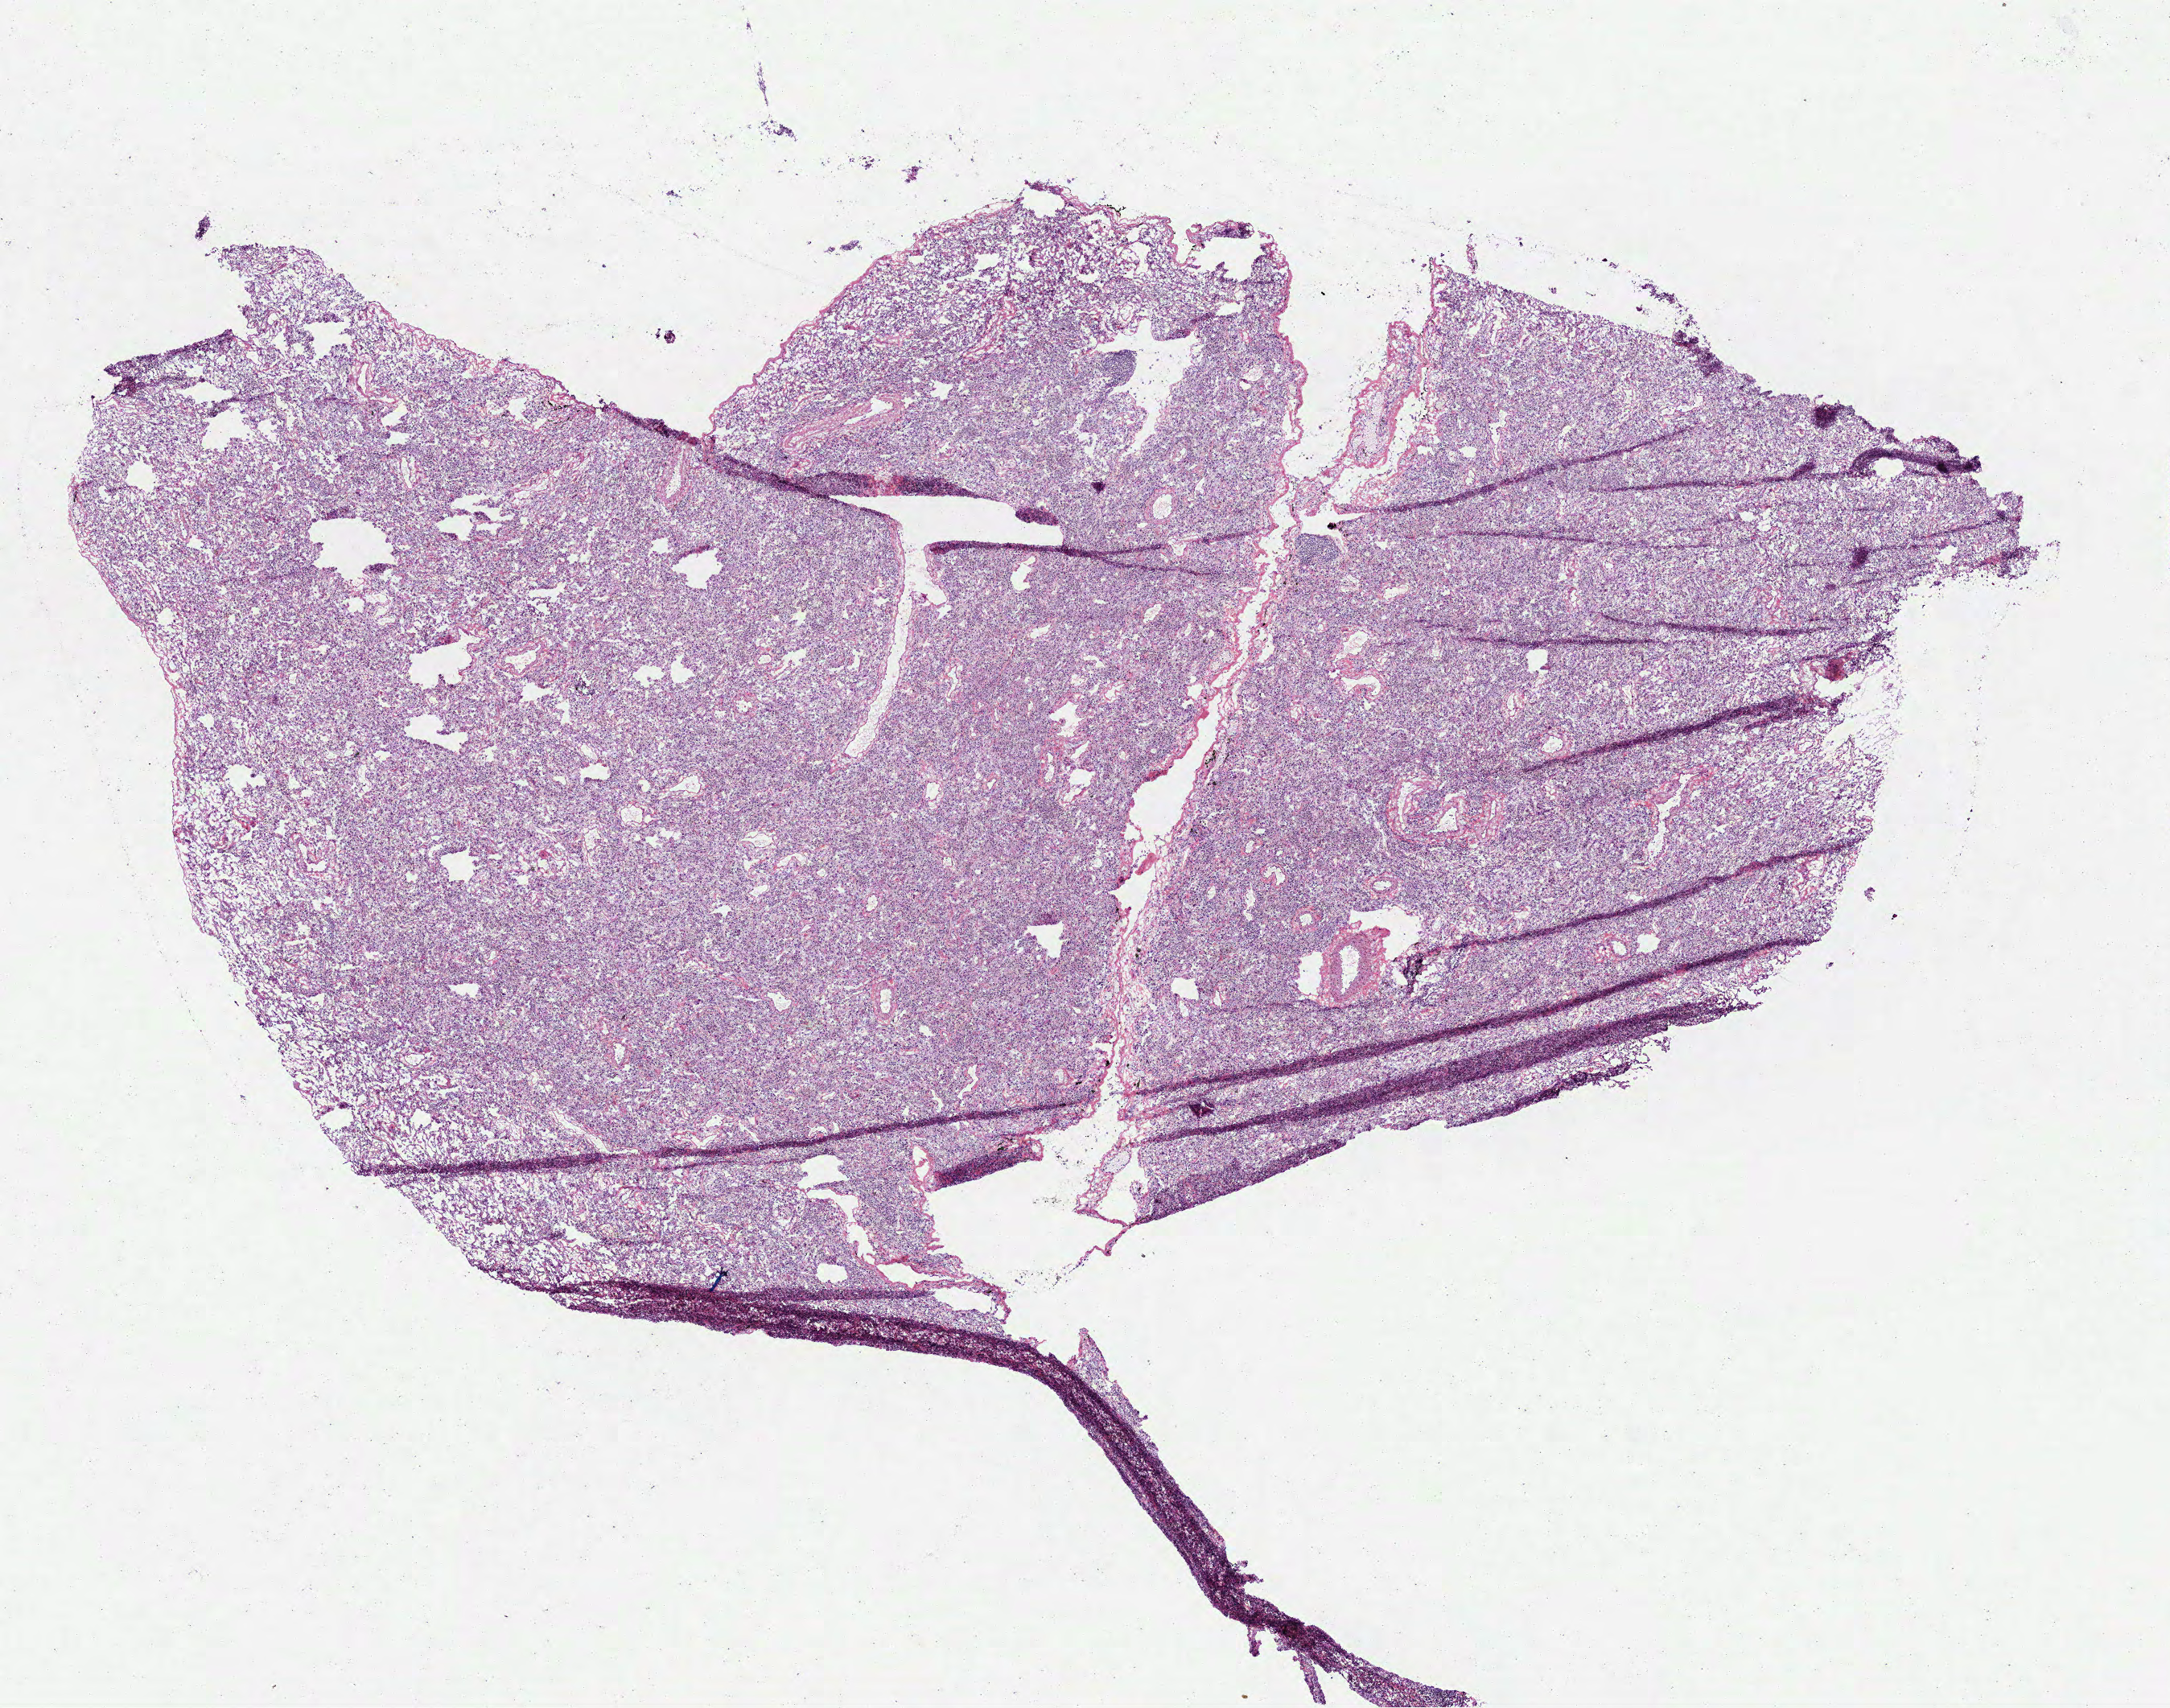
Digitized H&E-stained tissue section (whole slide) — shown as a low-resolution overview of the whole scanned area (about 10.9 x 8.6 mm, slide scanned at 40x); frozen section from the top of the tissue portion; sample: solid tissue normal (non-tumour tissue), lung. Female, age 70 years at initial diagnosis.
This section: solid tissue normal (non-tumour) sample from the same patient. Patient diagnosis: Adenocarcinoma, NOS (middle lobe, lung).